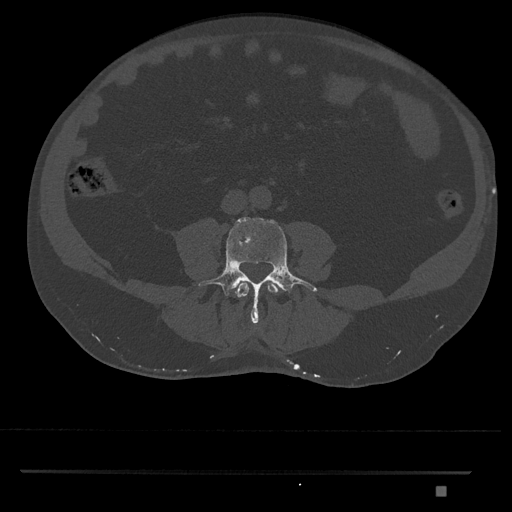
CT including the spine, one axial slice; position 630 of 1134 along the scan axis; reconstruction kernel Br40s/3; 120 kVp; bone window (W 1800 / L 400 HU); 0.5 mm slice thickness; 512 × 512 image matrix, field of view 429 × 429 mm. Patient: male, 65 years. Case-level facts recorded for this patient, not image findings: primary cancer: prostate.
Annotated regions visible in this slice (semi-automatically segmented with operator editing):
- L3 vertebra: box from (x=235, y=281) to (x=279, y=298) px
- L4 vertebra: (x=198, y=217)–(x=317, y=324)